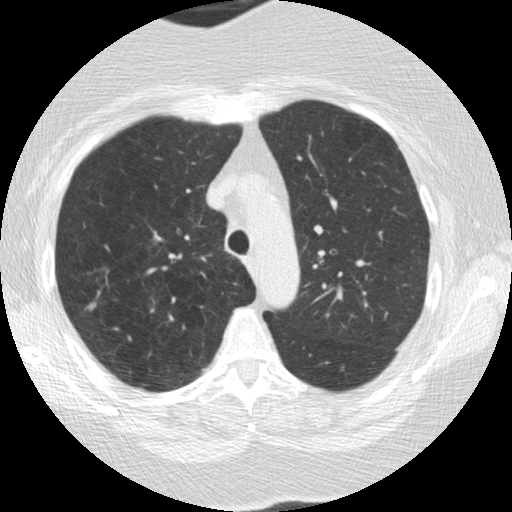
Low-dose screening chest CT, one axial slice. 120 kVp. Lung window (W 1500 / L -600 HU). 512 × 512 image matrix.
Outlined on this slice (manually delineated by an expert):
- lesion 1 (tumor, upper lobe of right lung): bounding box (x1, y1, x2, y2) in pixels: (86, 301, 98, 311)